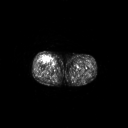
FDG PET of an extremity soft-tissue mass (from a PET/CT study), one axial slice. Slice 265 of 311 in the series (ordered by position). 3.27 mm slice thickness. 128 × 128 image matrix, field of view 700 × 700 mm. Male patient, age 56 years. Case-level facts recorded for this patient, not image findings: histological type: pleiomorphic leiomyosarcoma; grade: intermediate; site of the primary tumour: right thigh.
Structures marked on this image (expert contour drawn on MRI and transferred to this co-registered scan by the dataset authors):
- gross tumour volume including surrounding oedema: bounding box [x1, y1, x2, y2] px = [40, 55, 51, 62]
- gross tumour volume (mass): [43, 56, 50, 62]